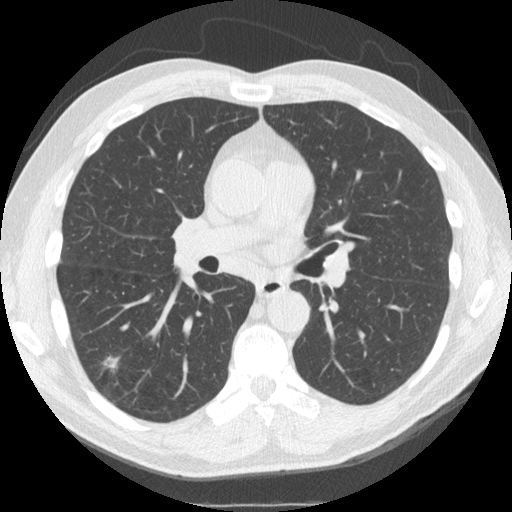
Low-dose screening chest CT, one axial slice; position 90 of 162 along the scan axis; lung window (W 1500 / L -600 HU); 2.5 mm slice thickness; 512 × 512 image matrix.
Structures marked on this image (expert manual segmentation):
- lesion 1 (nodule, lower lobe of right lung): box from (x=102, y=356) to (x=120, y=372) px